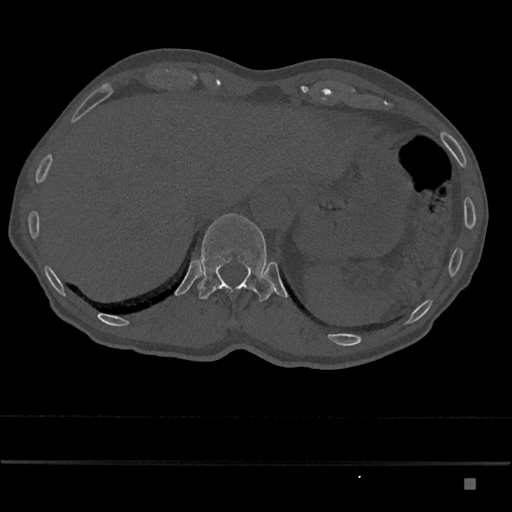
CT including the spine, one axial slice. Slice 623 of 797 in the series (ordered by position). 120 kVp. Bone window (W 1800 / L 400 HU). 0.5 mm slice thickness. 512 × 512 image matrix, field of view 390 × 390 mm. Male patient, age 72 years. From the clinical record (not read from this slice): primary cancer: prostate.
Annotated regions visible in this slice (semi-automatically segmented with operator editing):
- T12 vertebra: bounding box [x1, y1, x2, y2] px = [197, 213, 274, 302]